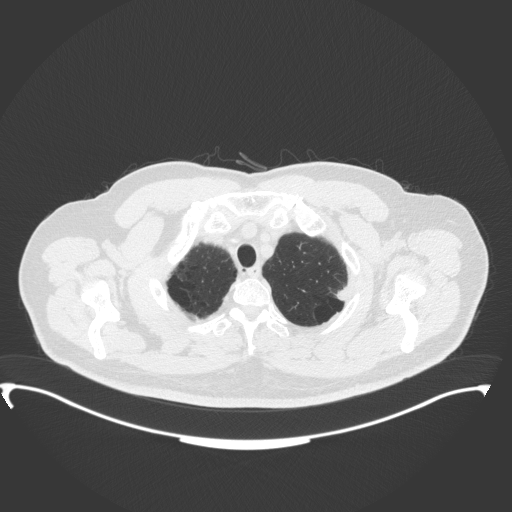
Chest CT, one axial slice. Slice 328 of 350 in the series (ordered by position). Lung window (W 1500 / L -600 HU). 512 × 512 image matrix, field of view 459 × 459 mm. Patient: male, 64 years. From the clinical record (not read from this slice): clinical TNM (as recorded): T1c N1 M1.
Outlined on this slice (bounding box drawn by a radiologist):
- lung tumour (recorded histology: adenocarcinoma): bounding box <335,282,352,305> (left, top, right, bottom; pixels)